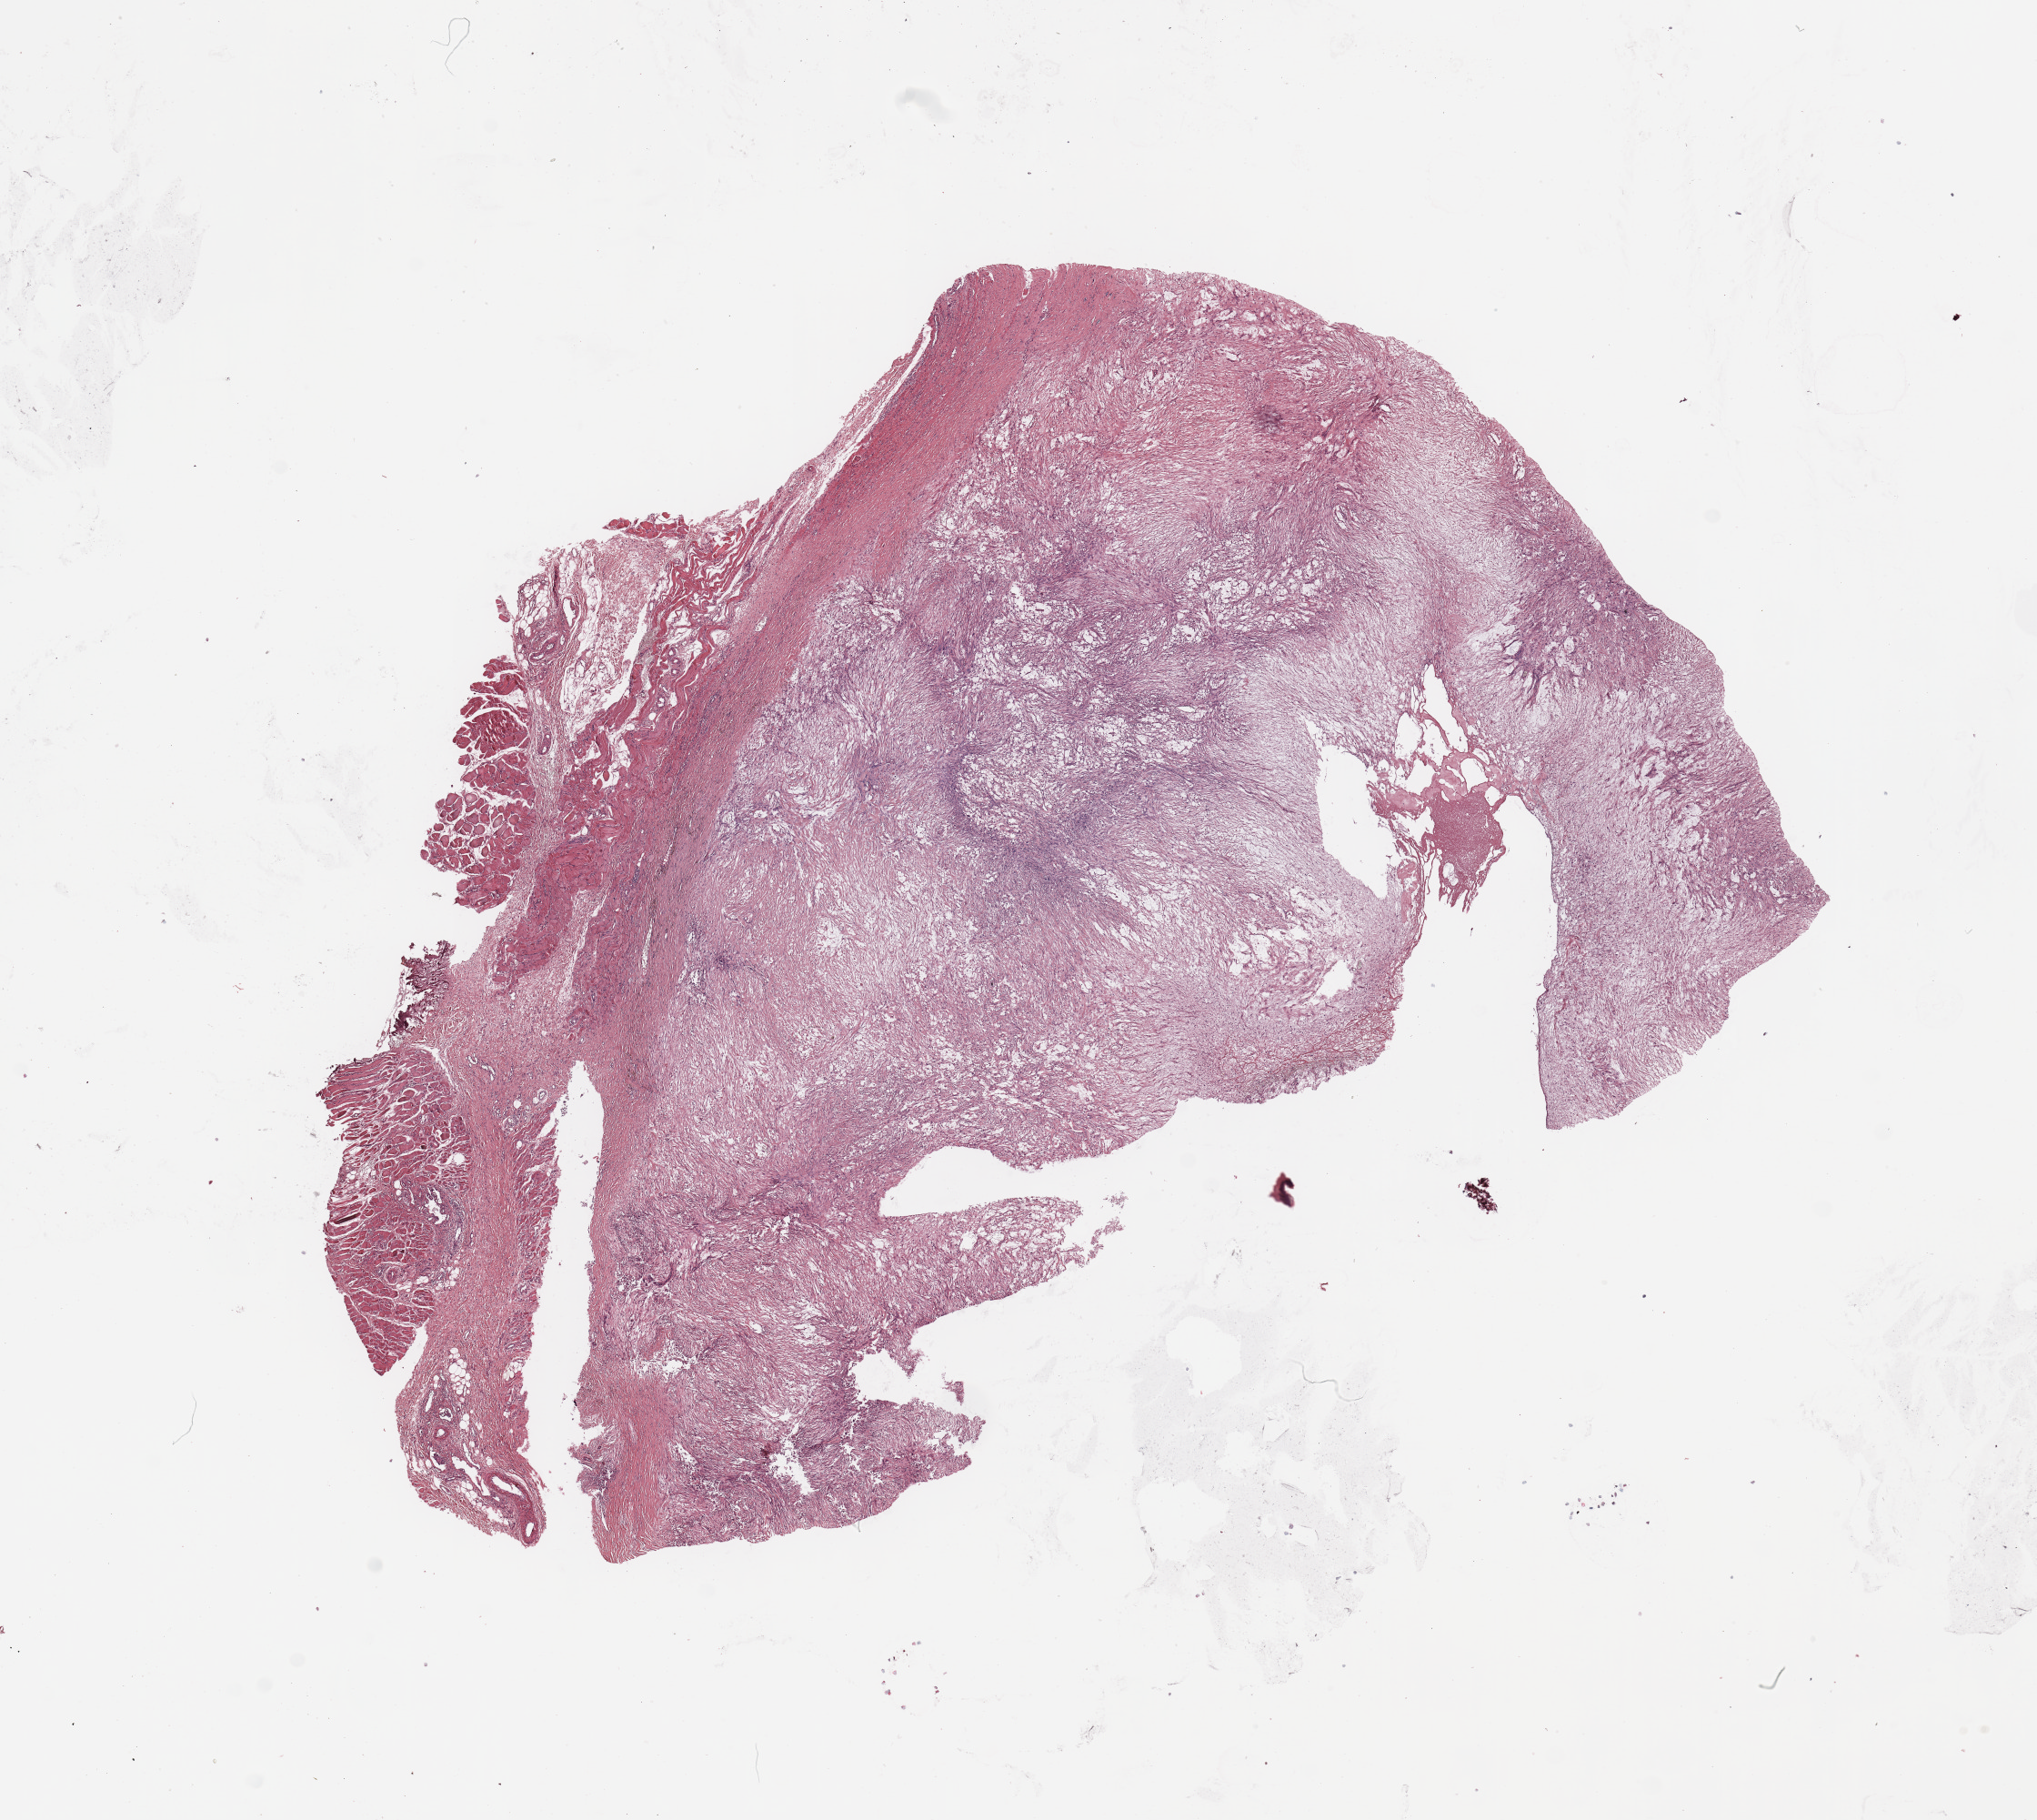
Digitized H&E tissue section (whole slide) — whole scanned area (about 17.7 x 15.8 mm, from a 20x scan) shown as a low-resolution overview; tumour tissue sample. Female, 67 y/o.
Patient diagnosis (cohort enrolment): sarcoma (site not recorded at cohort level). Primary tumour site (as recorded): superficial trunk.